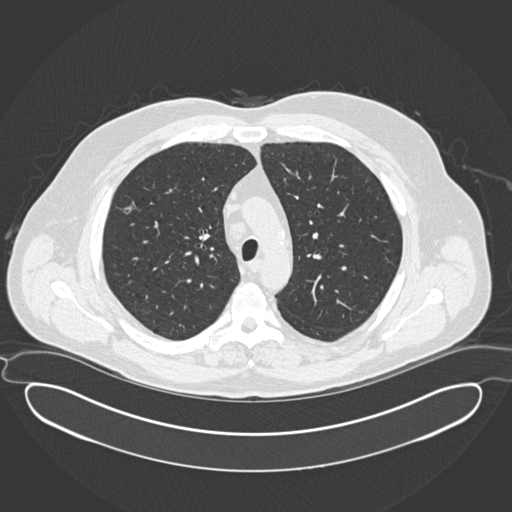
Low-dose screening chest CT, one axial slice; position 121 of 169 along the scan axis; lung window (W 1500 / L -600 HU); 2 mm slice thickness; 512 × 512 image matrix.
Annotated regions visible in this slice (outlined manually by an expert reader):
- lesion 1 (tumor, upper lobe of right lung): bounding box [x1, y1, x2, y2] px = [124, 202, 135, 214]